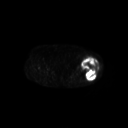
FDG PET of an extremity soft-tissue mass (from a PET/CT study), one axial slice. Slice 232 of 267 in the series (ordered by position). 3.27 mm slice thickness. 128 × 128 image matrix, field of view 700 × 700 mm. Patient: female, 62 years. From the clinical record (not read from this slice): histological type: undifferentiated – high grade; grade: high; site of the primary tumour: left thigh.
Structures marked on this image (expert contour drawn on MRI and transferred to this co-registered scan by the dataset authors):
- gross tumour volume including surrounding oedema: bounding box (x1, y1, x2, y2) in pixels: (81, 56, 99, 80)
- gross tumour volume (mass): (81, 56, 99, 80)